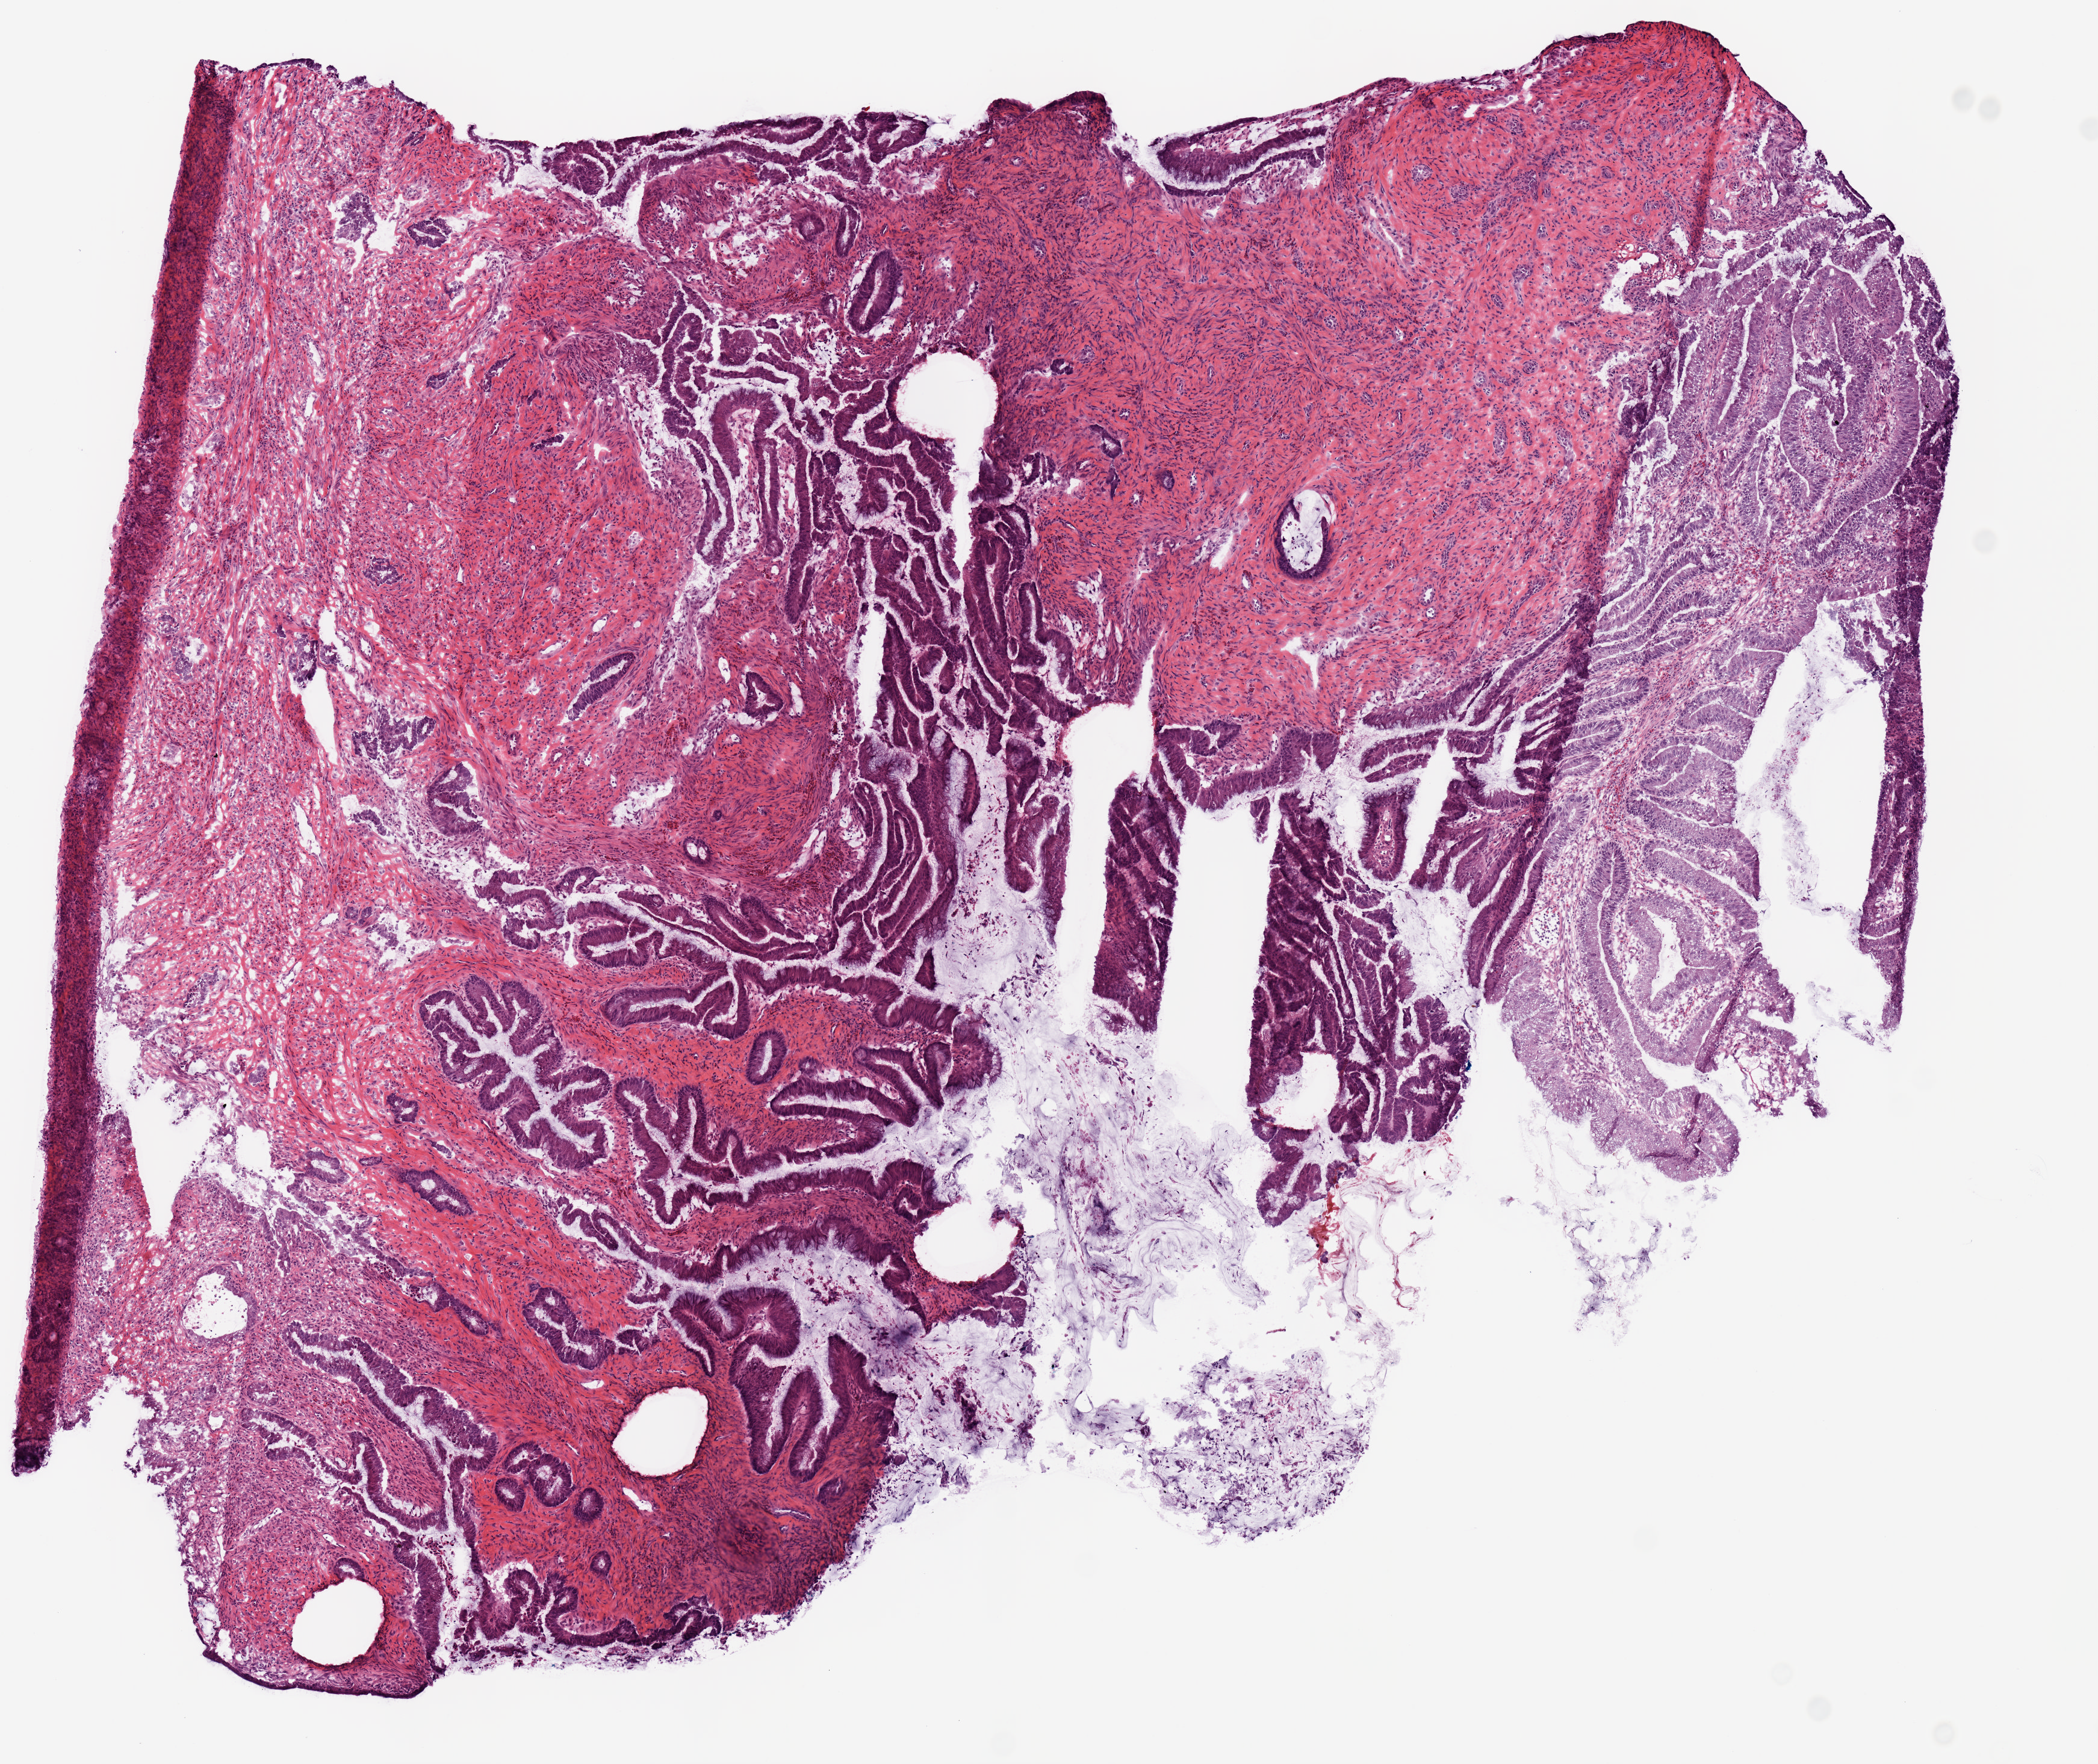
H&E whole-slide image — a low-resolution overview of the entire scanned area, about 6.9 x 5.8 mm; frozen section; primary tumour sample from the pancreas. Patient: male, age at initial diagnosis 77 years. Histologic grade: G1 (well differentiated). Composition of this section per pathologist review: tumour cells 40%, tumour nuclei 65%, normal cells 0%, stromal cells 60%, necrosis 0%.
• AJCC pathologic stage: IIB (7th edition)
• histologic diagnosis: Adenocarcinoma, NOS
• lymph nodes positive (case pathology): 1 of 9 examined
• TNM: T3 N1 MX